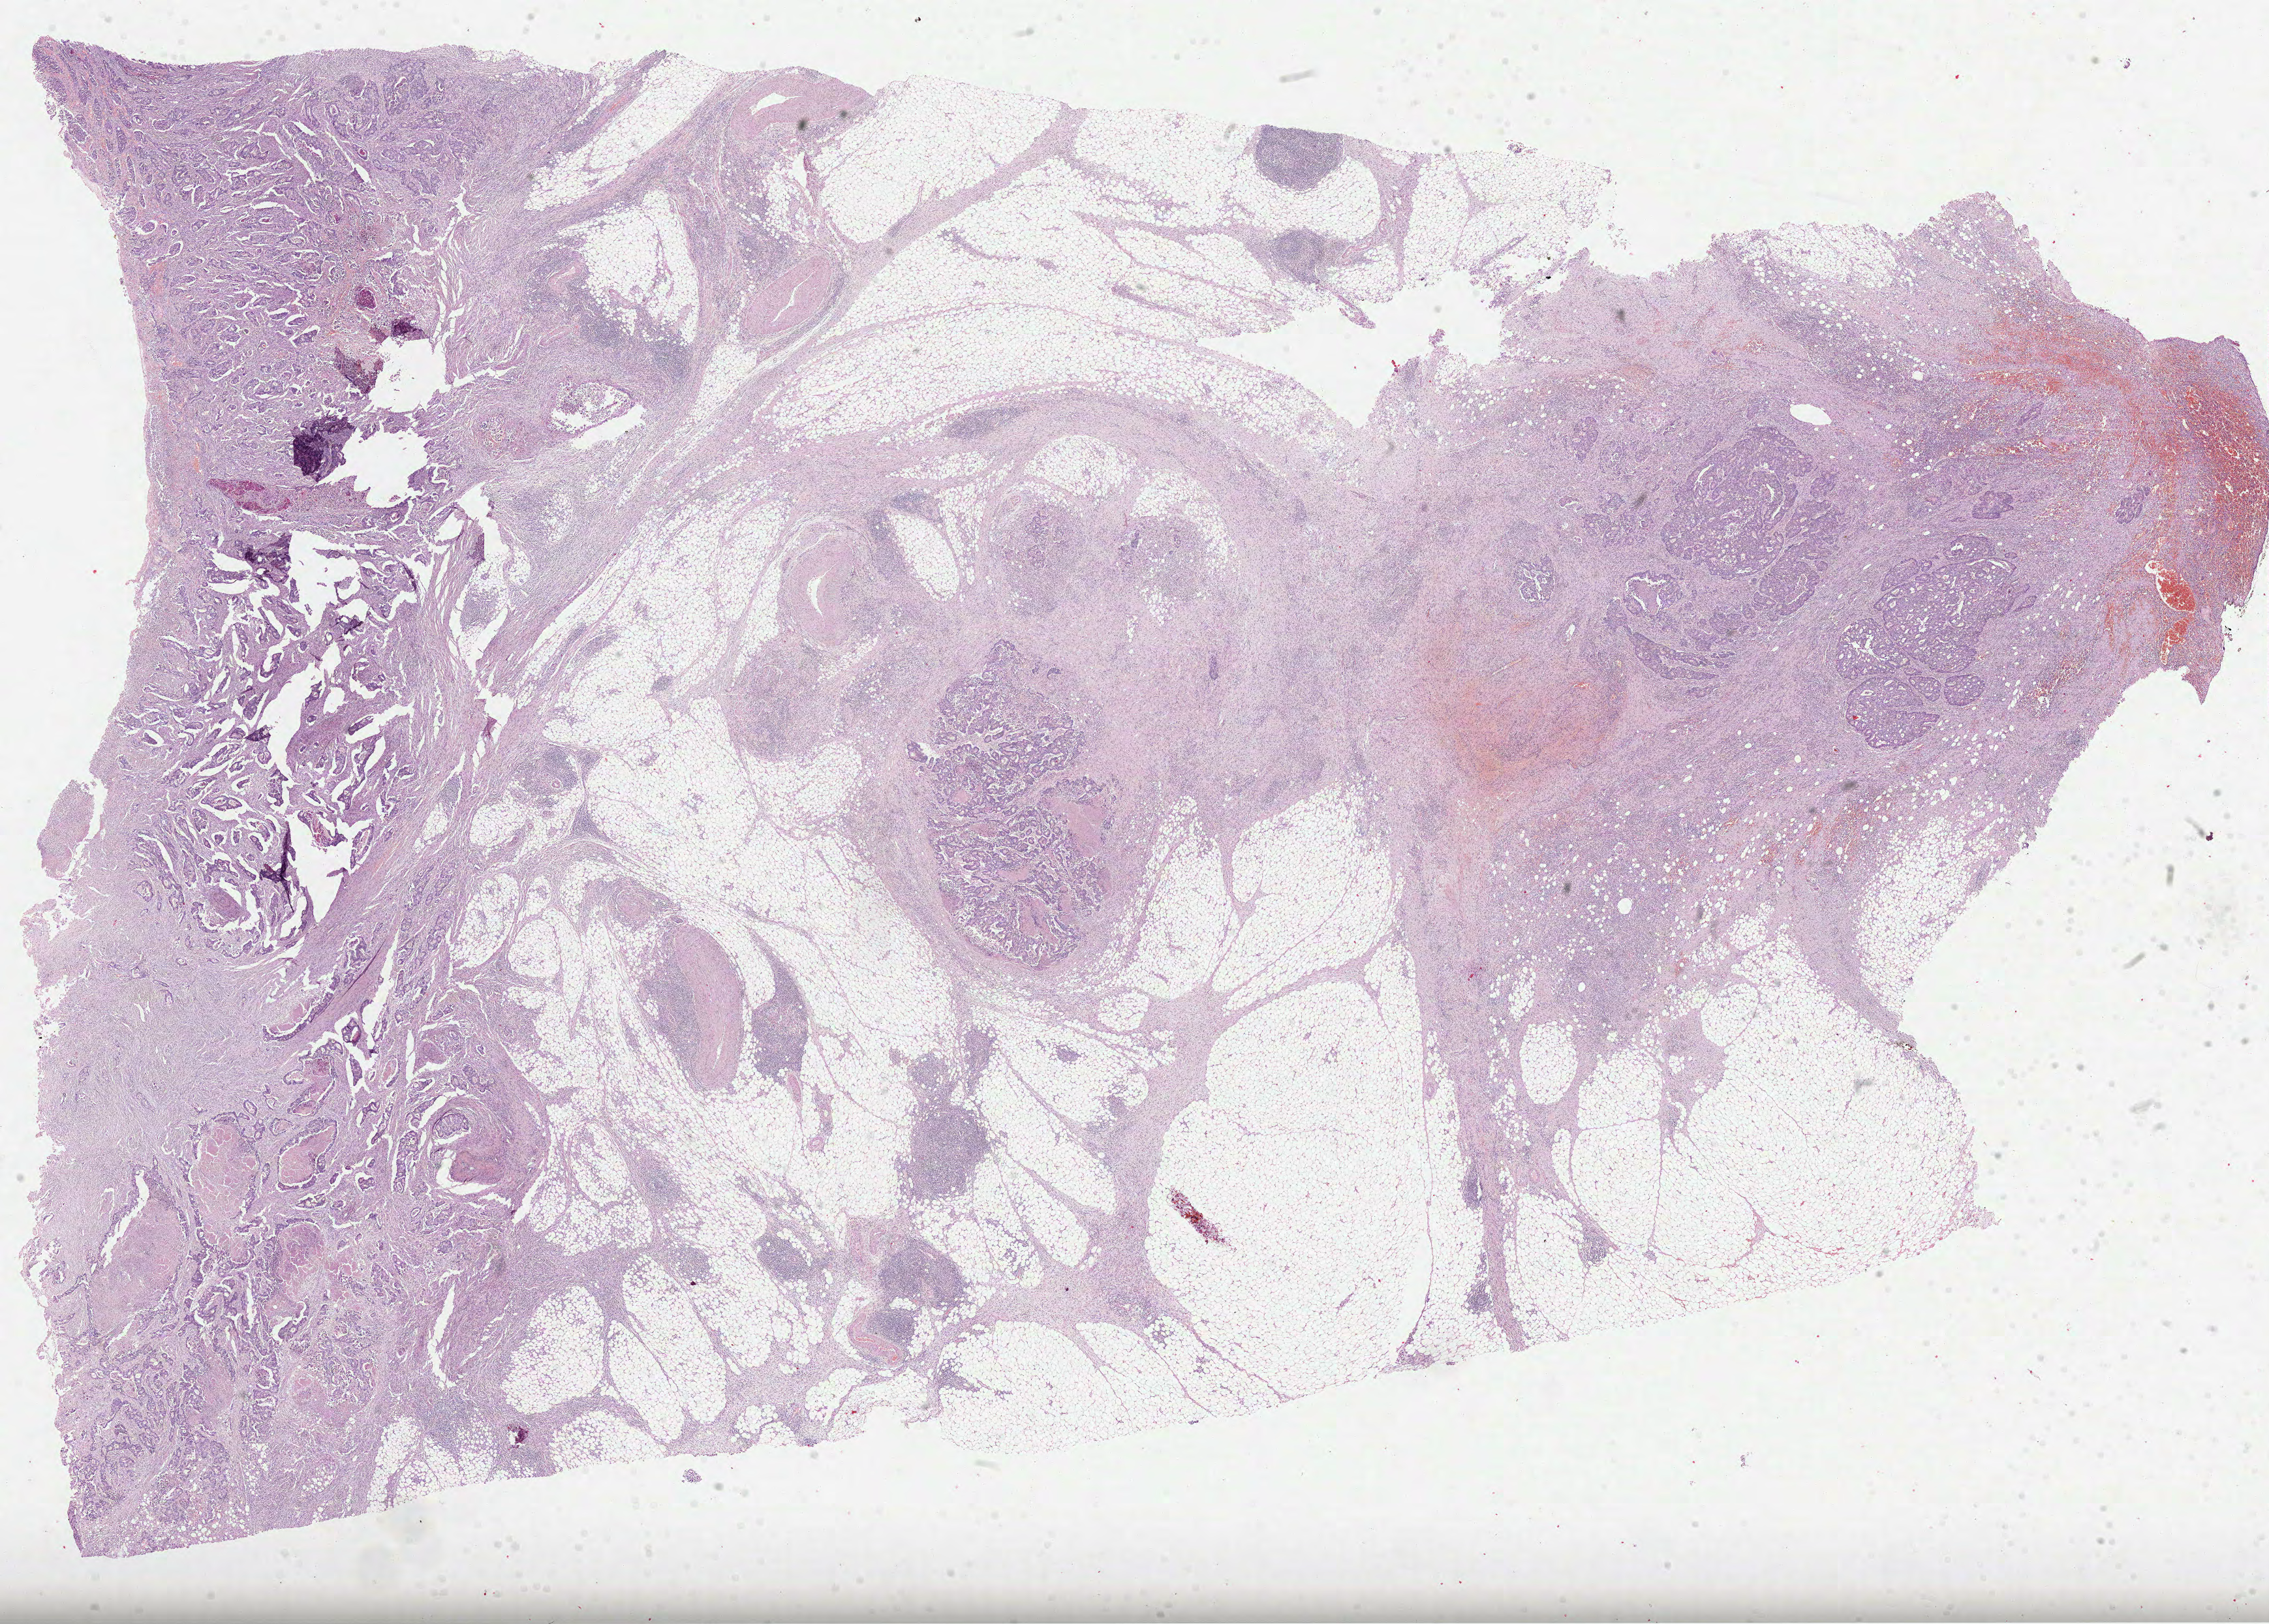
H&E-stained whole-slide image — shown as a low-resolution overview of the whole scanned area (about 28.0 x 20.1 mm), FFPE section, sample: primary tumour, rectum. Patient: female, age at initial diagnosis 64 years.
Pathologic diagnosis: Adenocarcinoma in tubulovillous adenoma.